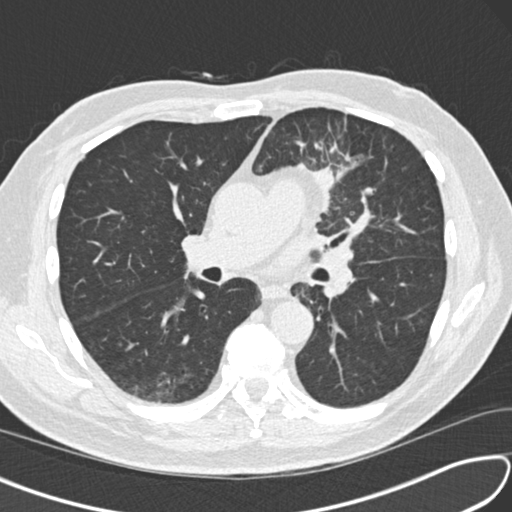
Low-dose screening chest CT, one axial slice. Slice 85 of 156 in the series (ordered by position). Reconstruction kernel B30f. 120 kVp. Lung window (W 1500 / L -600 HU). 2 mm slice thickness. 512 × 512 image matrix, field of view 340 × 340 mm.
Outlined on this slice (outlined manually by an expert reader):
- lesion 1 (tumor, upper lobe of left lung): box from (x=301, y=165) to (x=332, y=213) px